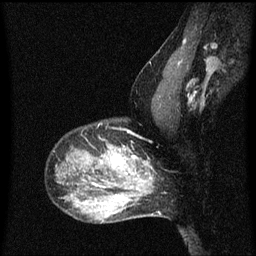
Breast MRI (dynamic contrast-enhanced), one sagittal slice; position 44 of 60 along the scan axis; dynamic contrast-enhanced series, image 2 of 3 at this slice position (ordered by acquisition); 1.5 T; TE 4.2 ms, TR 8 ms; 256 × 256 image matrix, field of view 200 × 200 mm. Patient: female, 50 years.
Structures marked on this image (semi-automatic segmentation, software-assisted and operator-edited):
- analysis volume of interest (the breast-tissue region the enhancement analysis was run in; not a lesion): bounding box <91,144,141,189> (left, top, right, bottom; pixels)
- tumour enhancement mask (voxels above the 70 % enhancement threshold inside the analysis volume of interest): <112,150,136,171>